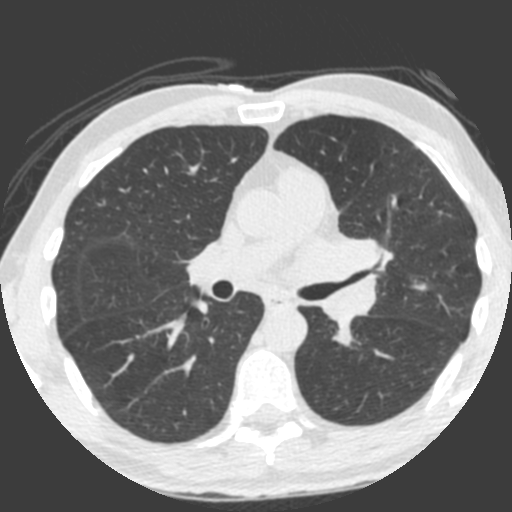
Low-dose screening chest CT, axial slice, third annual screen, lung window (W 1500 / L -600 HU), slice 128 of 212 in the series, 512 × 512 image matrix. Male participant, aged 55 years at enrolment. Current smoker at enrolment.
Expert reader's lesion annotation, bounding box [x1, y1, x2, y2] px = [309, 211, 401, 325]. The exam's reader record, not a measurement of the box and not confirmed to be the same lesion: non-calcified nodule or mass ≥4 mm, left upper lobe, 49 × 29 mm, spiculated (stellate) margins, soft tissue attenuation, pre-existing on the prior screen: yes; interval growth: yes. Lung cancer was diagnosed 0 days after this screen: small cell carcinoma, NOS, left upper lobe, undifferentiated (G4), stage IV (AJCC 6th edition), 60 mm at pathology.